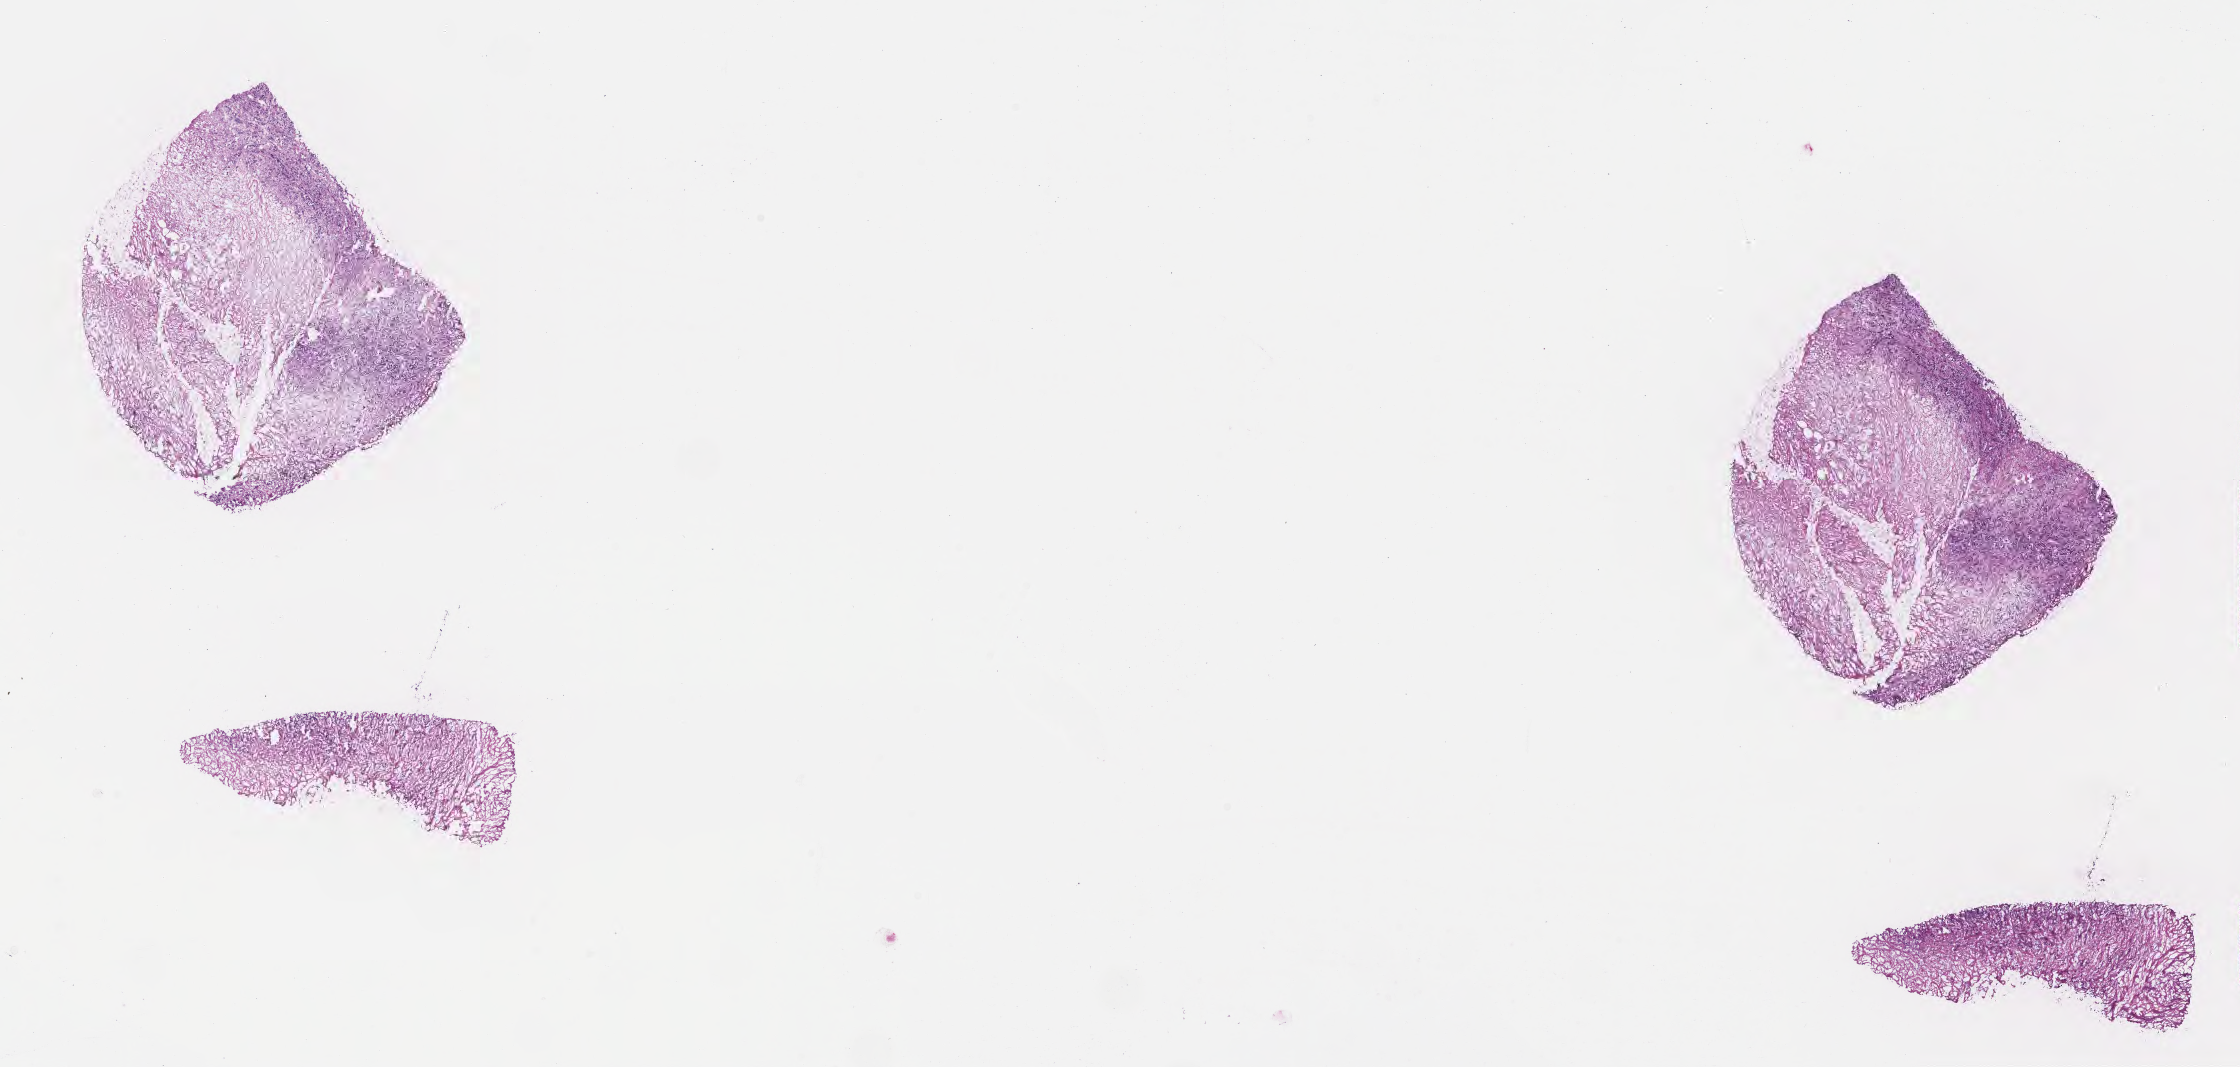
Haematoxylin and eosin whole-slide image, a low-resolution overview of the entire scanned area, about 18.1 x 8.6 mm; frozen section (tissue freezing medium); primary tumor; site: head of pancreas. Male, age 48 years at initial diagnosis. Tumor grade: G3 (poorly differentiated). Pathologist review of this section (percent, as recorded): tumor cells 25%, tumor nuclei 30%, stromal cells 75%, necrosis 0%, normal cells 0%. Inflammatory infiltration, as recorded: lymphocyte infiltration 0%, monocyte infiltration 0%, neutrophil infiltration 0%.
• section: bottom of the tissue portion
• histologic diagnosis: Infiltrating duct carcinoma, NOS
• AJCC pathologic stage: Stage IV